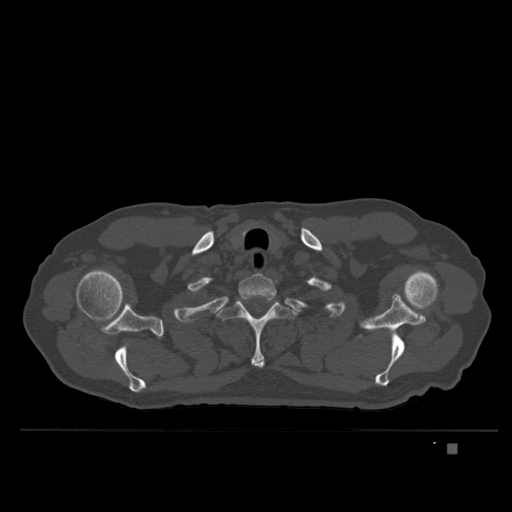
CT including the spine, one axial slice; slice 316 of 435 in the series (ordered by position); bone window (W 1800 / L 400 HU); 1.5 mm slice thickness; 512 × 512 image matrix, field of view 434 × 434 mm. Patient: male, 73 years. Case-level facts recorded for this patient, not image findings: primary cancer: skin.
Outlined on this slice (semi-automatic segmentation, software-assisted and operator-edited):
- T1 vertebra: bounding box (x1, y1, x2, y2) in pixels: (239, 273, 277, 297)
- T2 vertebra: (217, 295, 296, 368)